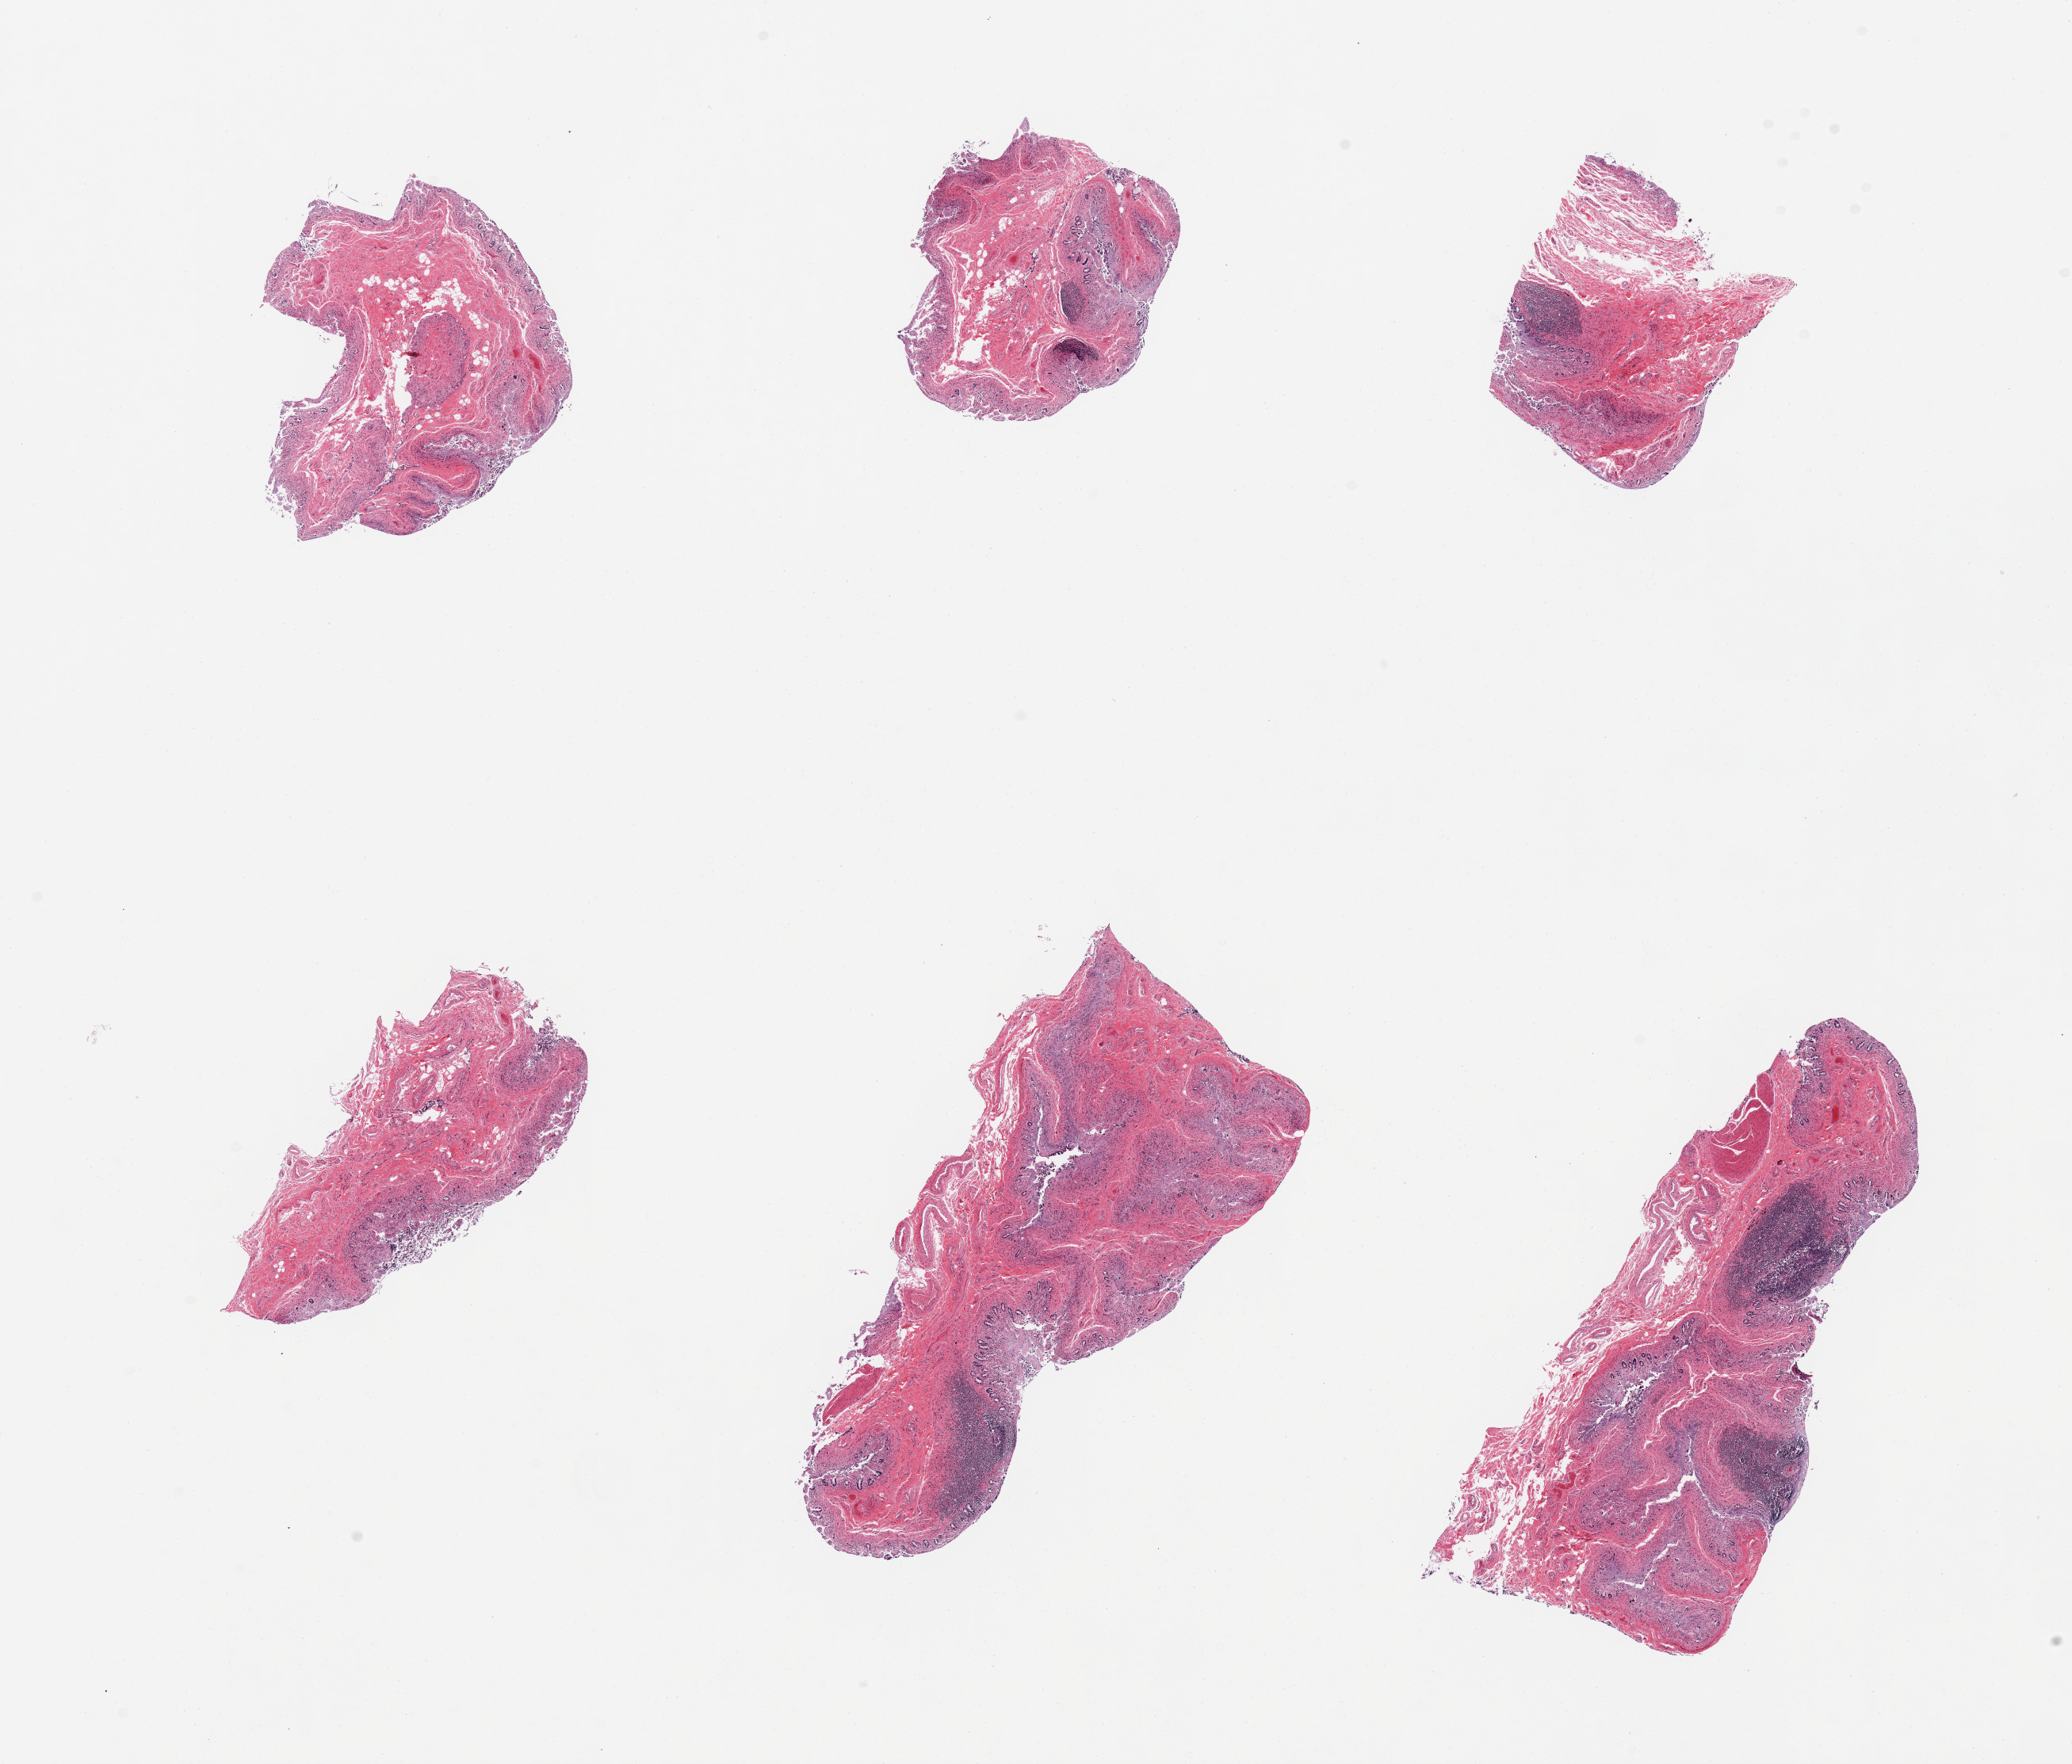
Whole-slide image, H&E stain, whole scanned area (about 20.7 x 17.6 mm, acquisition: 20x scan) shown as a low-resolution overview. Female donor.
- specimen: PAXgene-fixed, paraffin-embedded tissue; section of ileum (target tissue); tissue donor sample